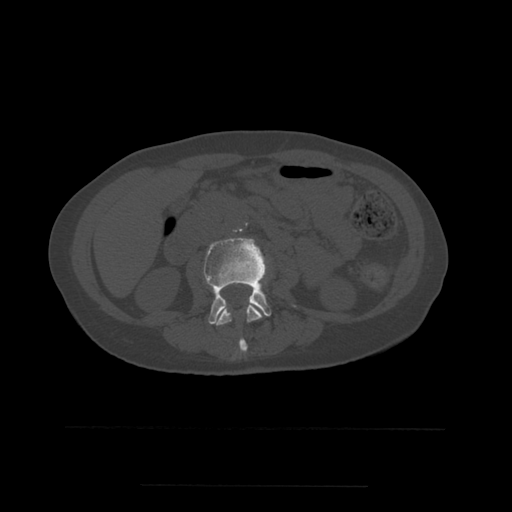
CT including the spine, one axial slice; position 197 of 544 along the scan axis; bone window (W 1800 / L 400 HU); 512 × 512 image matrix, field of view 350 × 350 mm. Patient age 58 years. Case-level facts recorded for this patient, not image findings: primary cancer: lung.
Annotated regions visible in this slice (semi-automatic segmentation, software-assisted and operator-edited):
- L2 vertebra: bounding box <217,300,263,353> (left, top, right, bottom; pixels)
- L3 vertebra: <204,238,272,326>